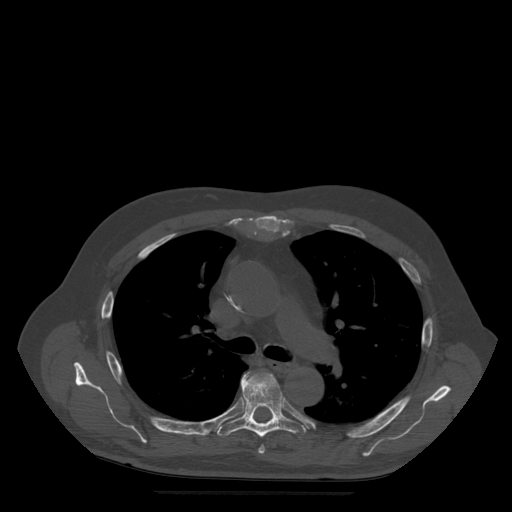
CT including the spine, one axial slice. Slice 357 of 522 in the series (ordered by position). Bone window (W 1800 / L 400 HU). 1.25 mm slice thickness. 512 × 512 image matrix. Patient age 72 years. Case-level facts recorded for this patient, not image findings: primary cancer: prostate.
Outlined on this slice (semi-automatically segmented with operator editing):
- T5 vertebra: box from (x=259, y=446) to (x=265, y=454) px
- T6 vertebra: (x=217, y=371)–(x=306, y=438)